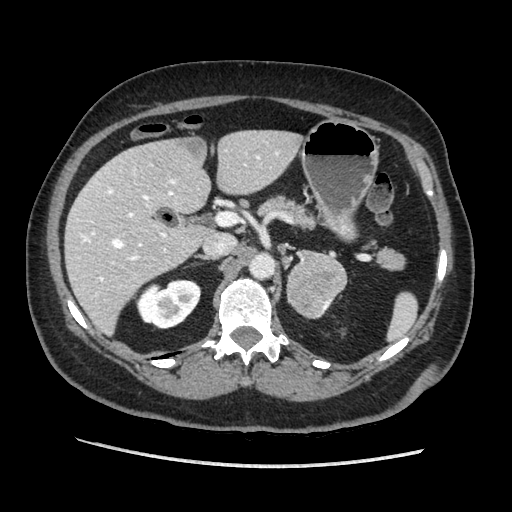
Contrast-enhanced abdominal CT, one axial slice; position 120 of 203 along the scan axis; soft-tissue window (W 400 / L 40 HU); 1.25 mm slice thickness; 512 × 512 image matrix, field of view 360 × 360 mm. Female patient. Case-level facts recorded for this patient, not image findings: diagnosis: adrenocortical carcinoma; tumour side: left adrenal; tumour size at pathology: 6.5 cm; Ki-67 index: 22 %; stage (as recorded): 2.
Structures marked on this image (semi-automatically segmented with operator editing):
- mass: bounding box (x1, y1, x2, y2) in pixels: (288, 254, 348, 318)